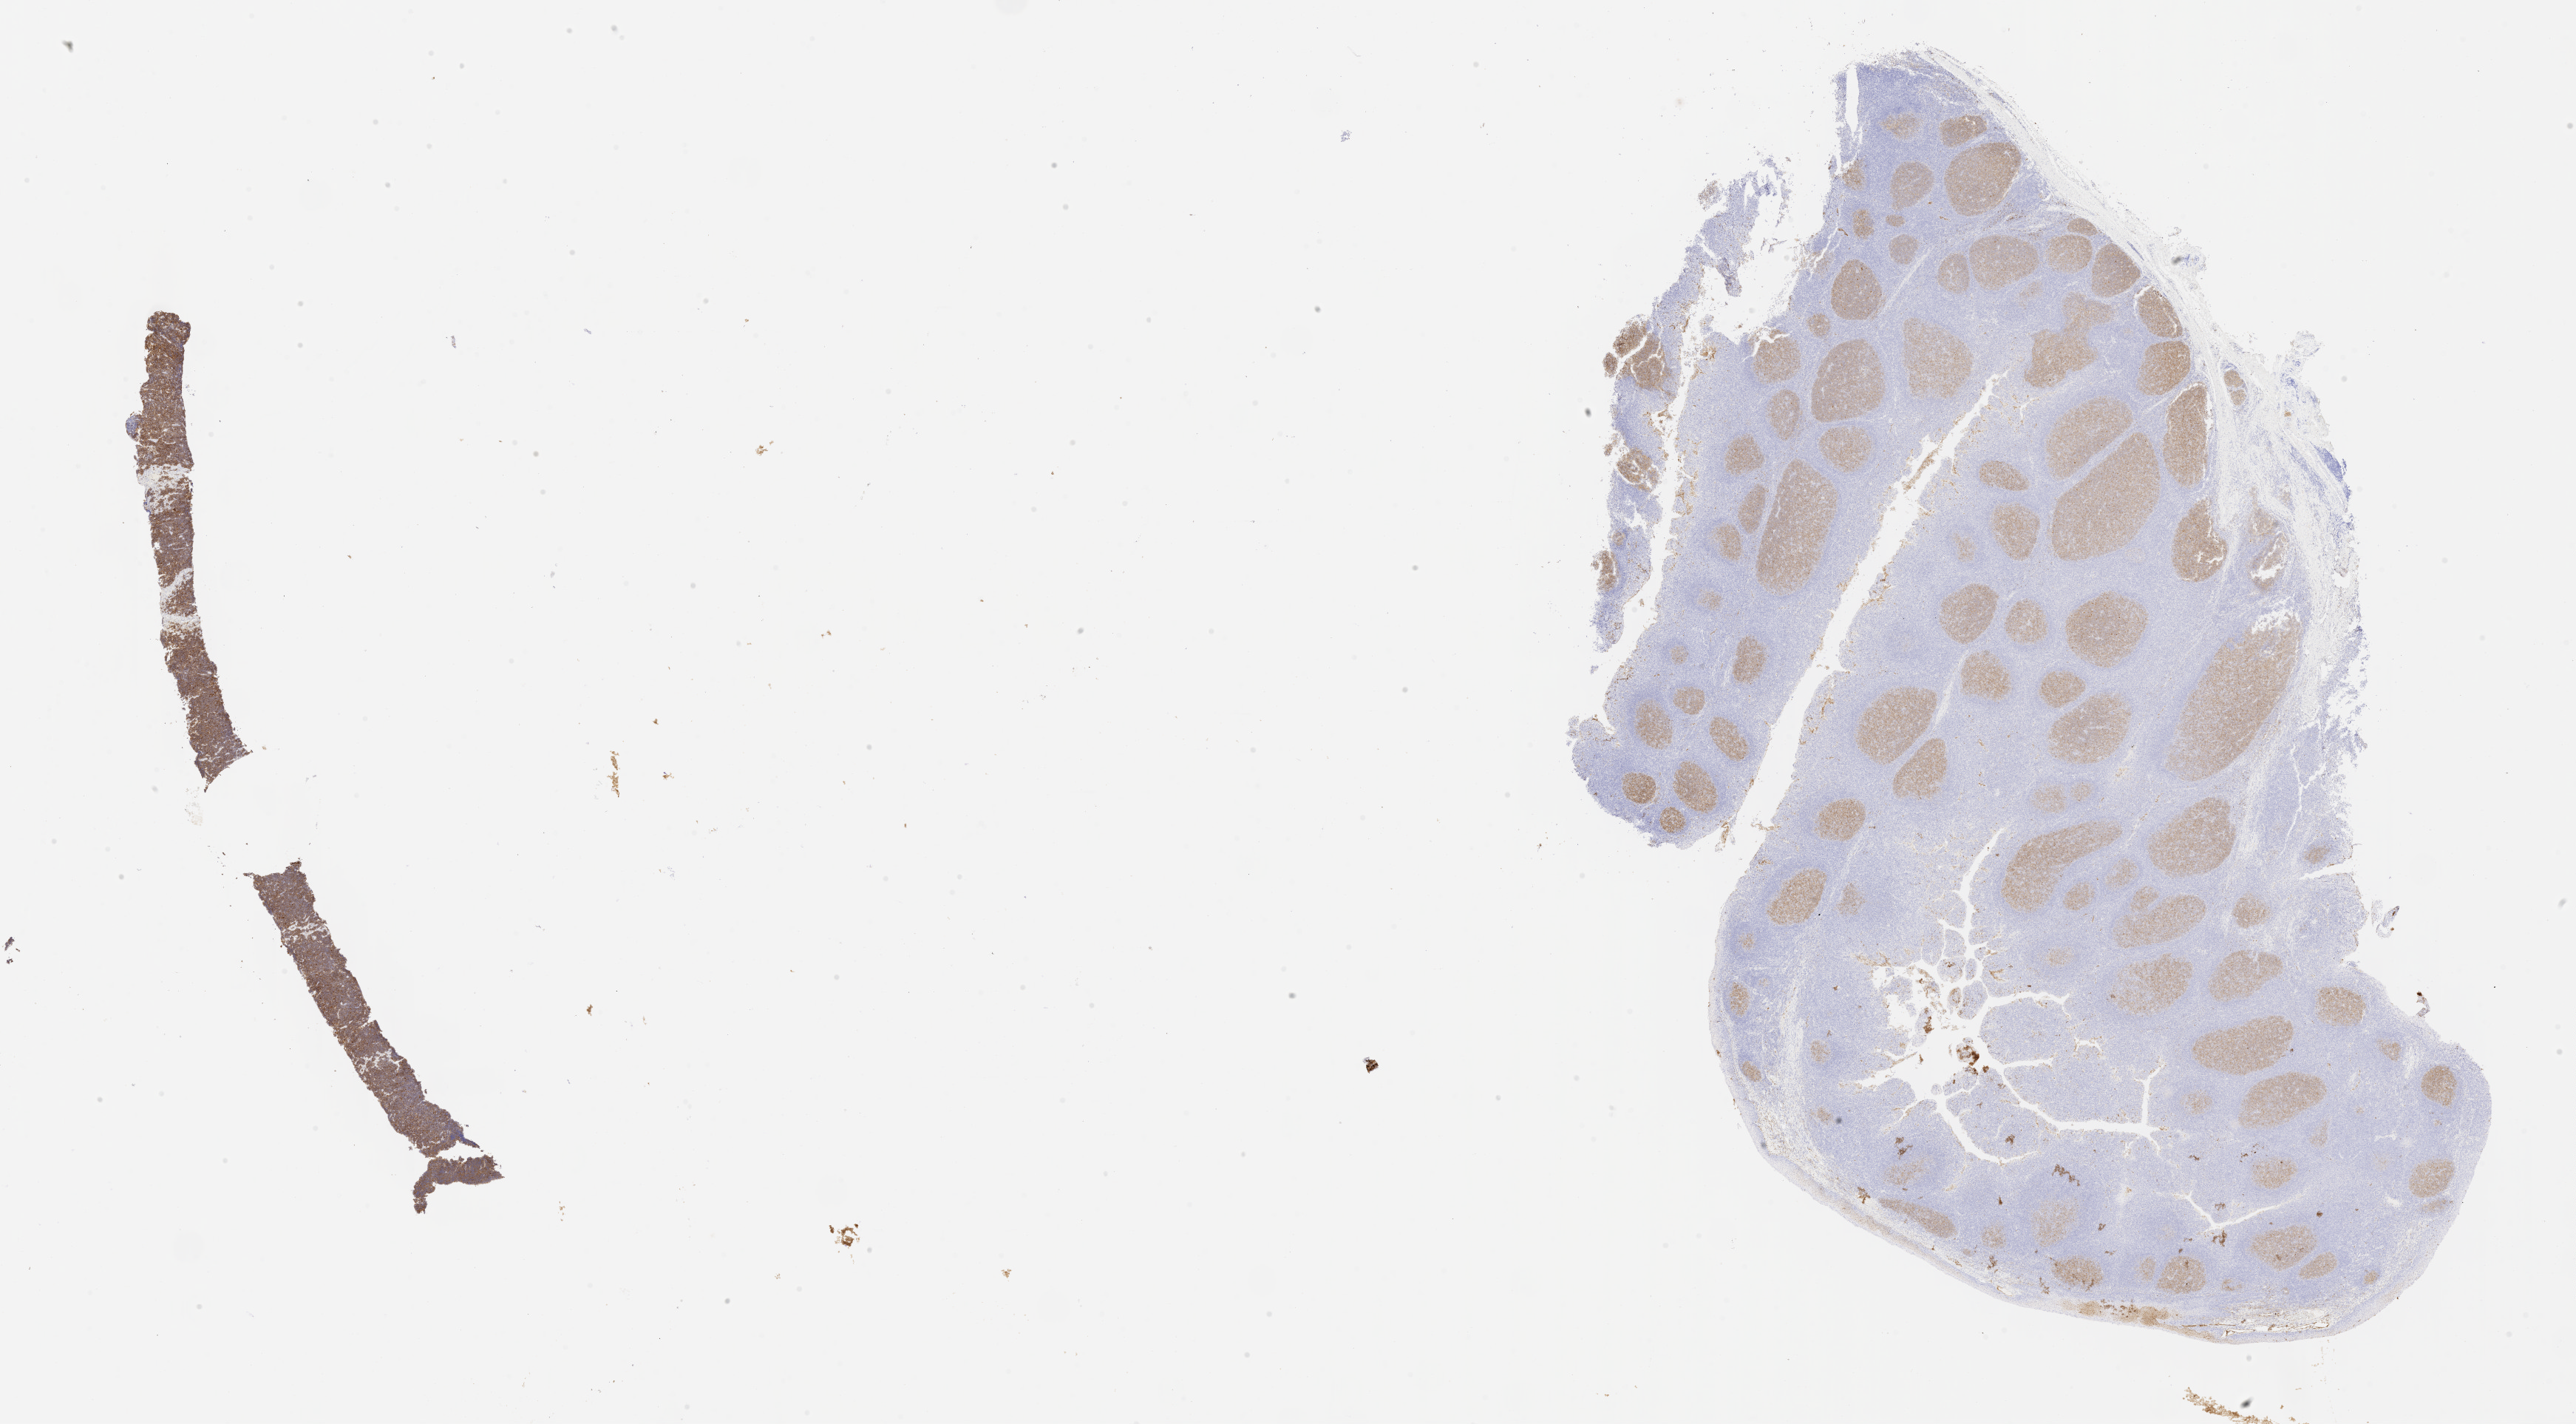
Whole-slide image, immunohistochemical stain for CD10, shown as a low-resolution overview of the whole scanned area (about 28.2 x 15.6 mm). Female patient.
Specimen: tumor tissue.